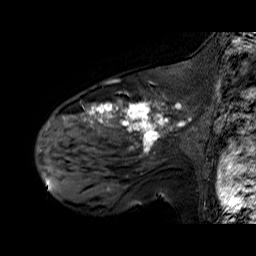
Breast MRI (dynamic contrast-enhanced), one sagittal slice; position 43 of 60 along the scan axis; dynamic contrast-enhanced series, time point 2 of 6 at this slice position (early post-contrast); 1.5 T; TE 6.3 ms, TR 32.9 ms; 4 mm slice thickness; 256 × 256 image matrix, field of view 200 × 200 mm. Female patient. Case-level facts recorded for this patient, not image findings: setting: breast cancer imaged before/during neoadjuvant chemotherapy; receptor status: HER2-positive.
Annotated regions visible in this slice (semi-automatic segmentation, software-assisted and operator-edited):
- analysis volume of interest (the breast-tissue region the enhancement analysis was run in; not a lesion): box from (x=48, y=92) to (x=195, y=174) px
- tumour enhancement mask (voxels above the 100 % enhancement threshold inside the analysis volume of interest): (x=63, y=99)–(x=185, y=150)